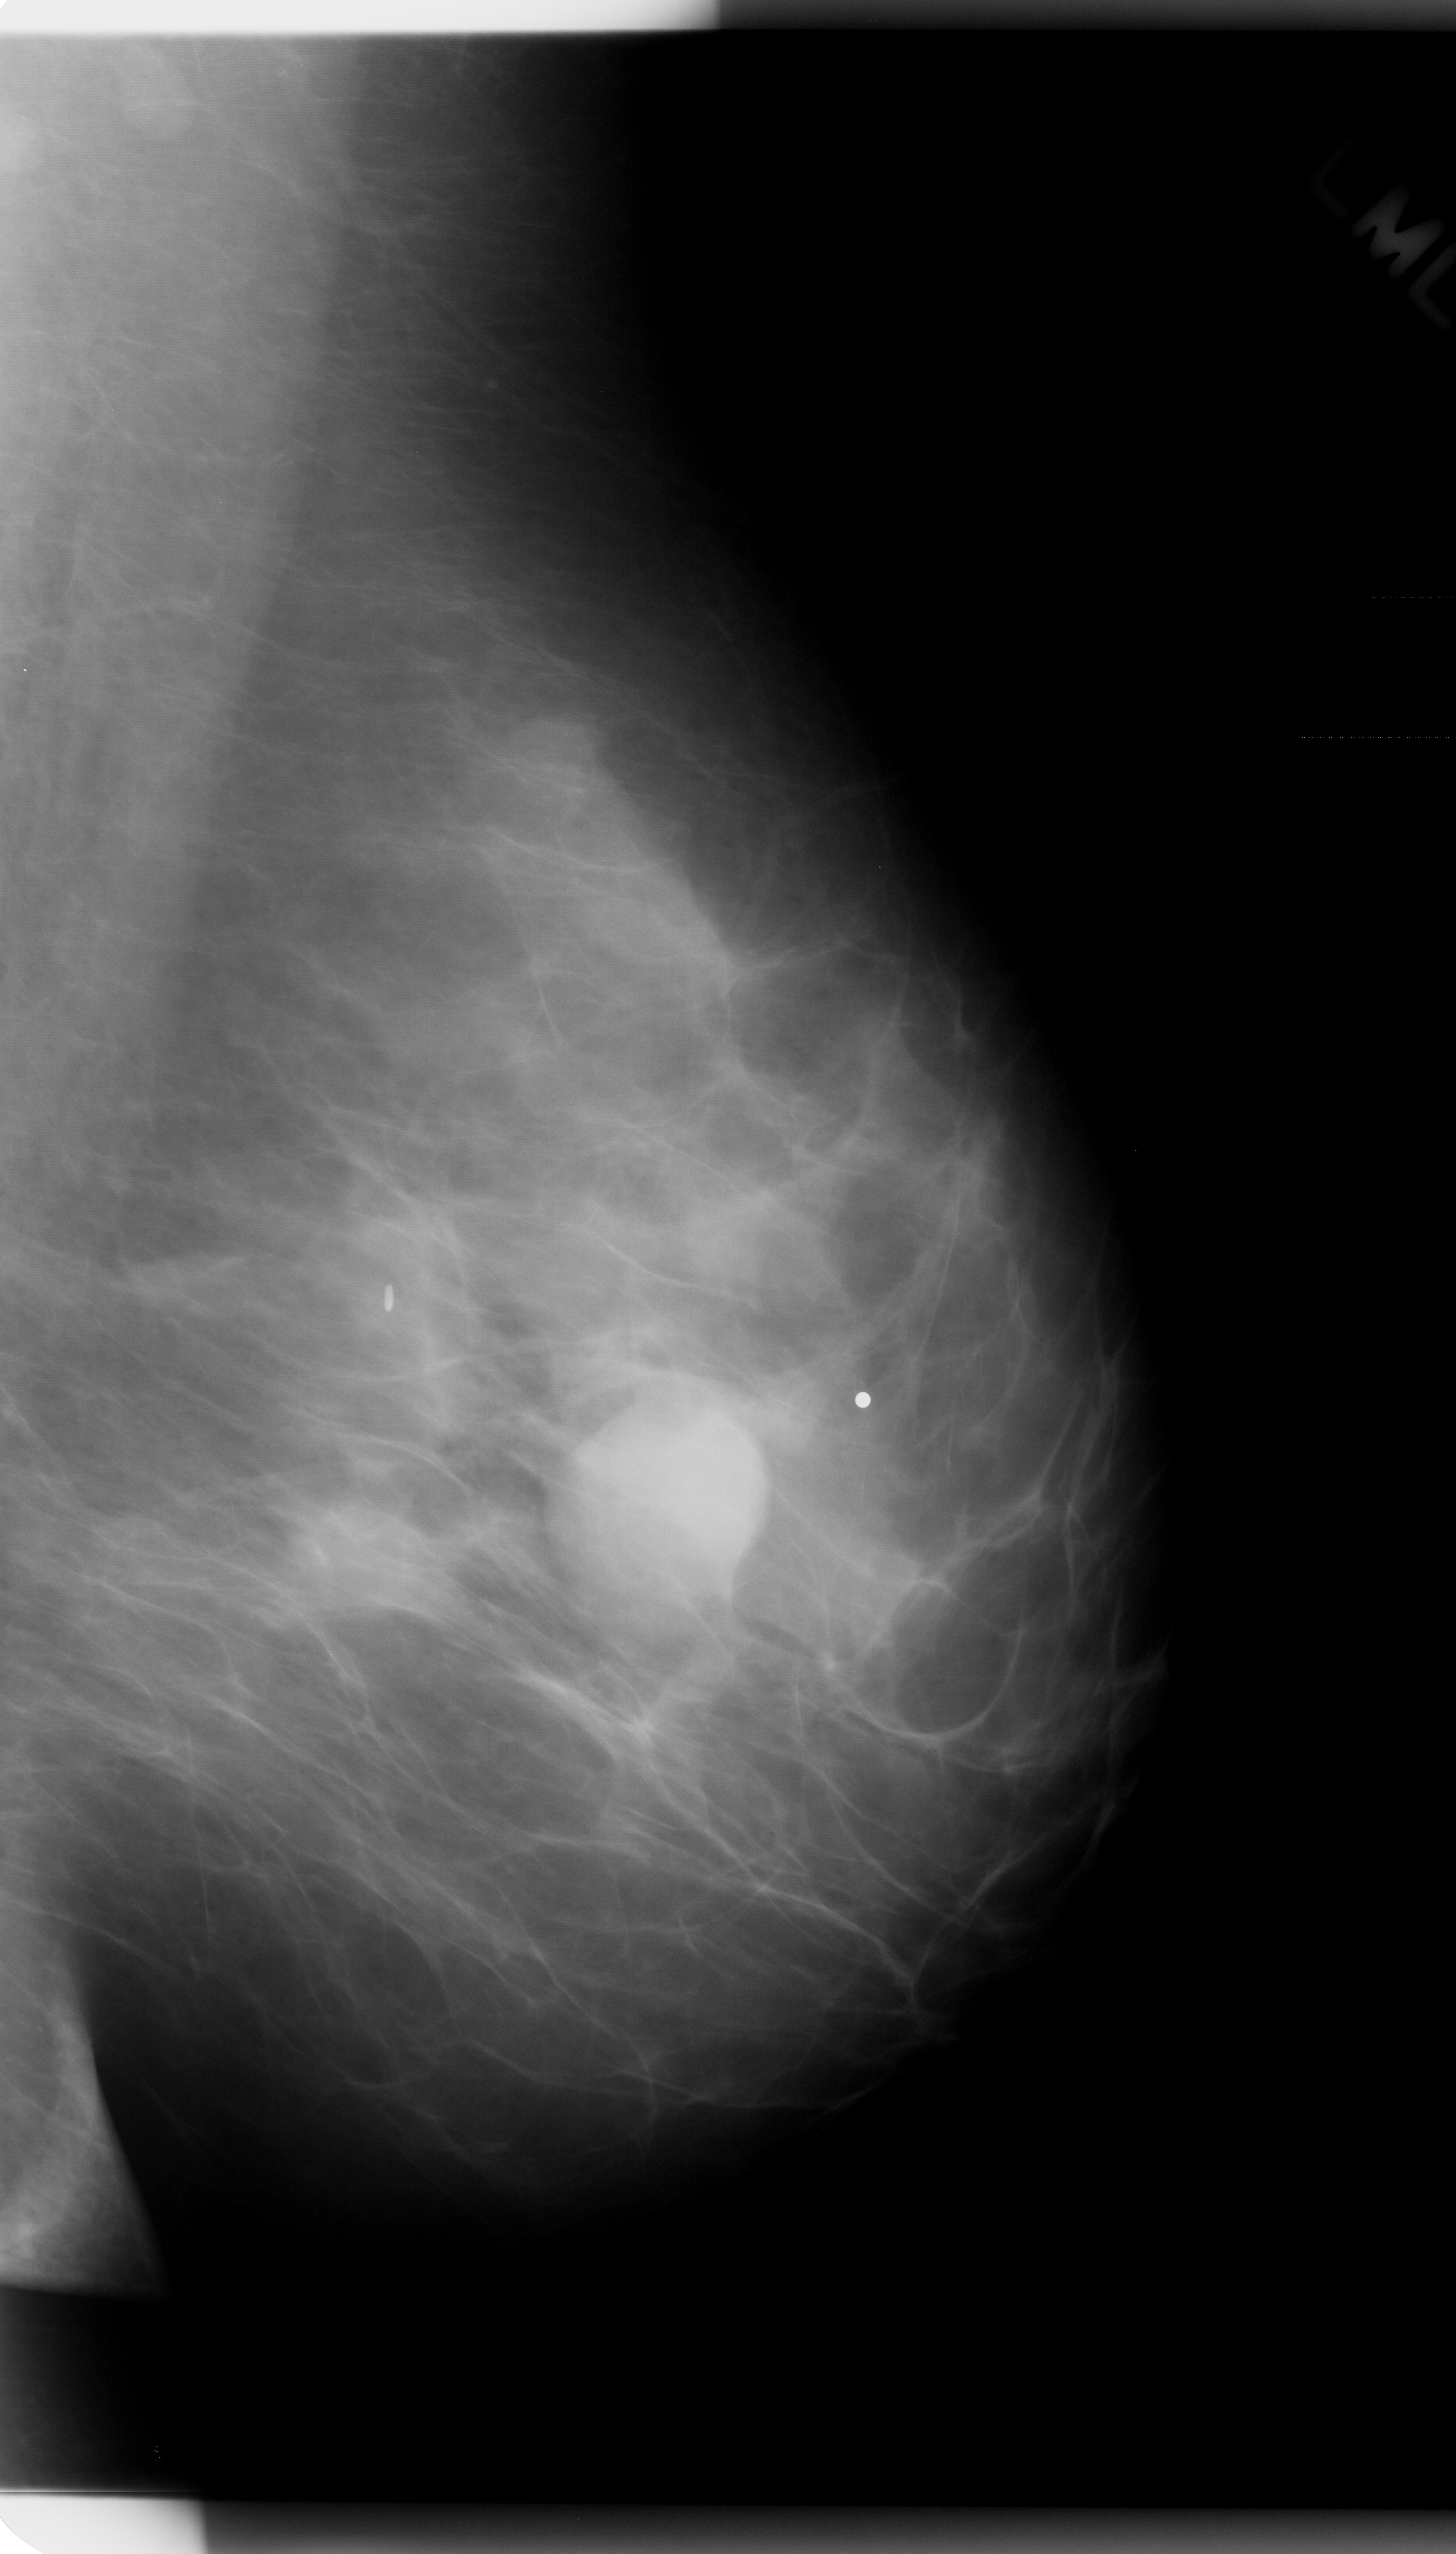
Scanned film-screen mammogram. Left breast. Mediolateral oblique (MLO) view. 1456 × 2554 image matrix.
Expert-marked regions of interest on this image (one box per marked abnormality):
- mass, shape round, margins obscured; BI-RADS assessment category 4; subtlety rating 5 on a 1 (subtle) to 5 (obvious) scale; pathology (as recorded): benign: bounding box [x1, y1, x2, y2] px = [510, 1353, 783, 1641]